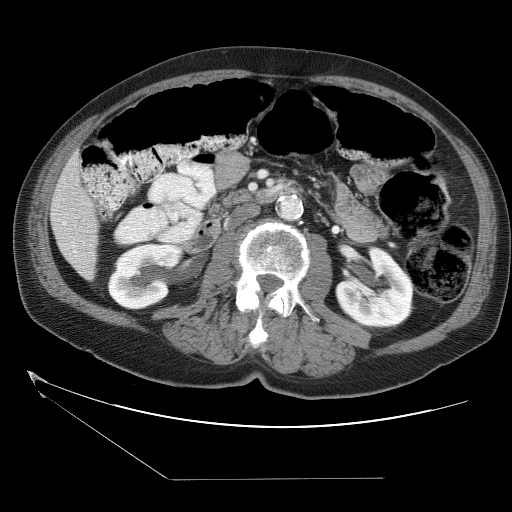
Contrast-enhanced abdominal CT (liver protocol), one axial slice. Slice 6 of 38 in the series (ordered by position). Reconstruction kernel STANDARD. 120 kVp. Soft-tissue window (W 400 / L 40 HU). 5 mm slice thickness. 512 × 512 image matrix, field of view 400 × 400 mm. From the clinical record (not read from this slice): diagnosis: hepatocellular carcinoma (patient treated with transarterial chemoembolisation; whether this scan precedes or follows treatment is not stated here); TNM stage (as recorded): Stage-II; Child-Pugh class: A; tumour differentiation: moderately differentiated; tumour size: 0.8 cm.
Annotated regions visible in this slice (semi-automatic segmentation, software-assisted and operator-edited):
- liver parenchyma outside the tumour (the mass and vessels are separate outlines, so this box may not span the whole liver): bounding box (x1, y1, x2, y2) in pixels: (50, 150, 98, 280)
- liver vessels: (58, 219, 66, 225)